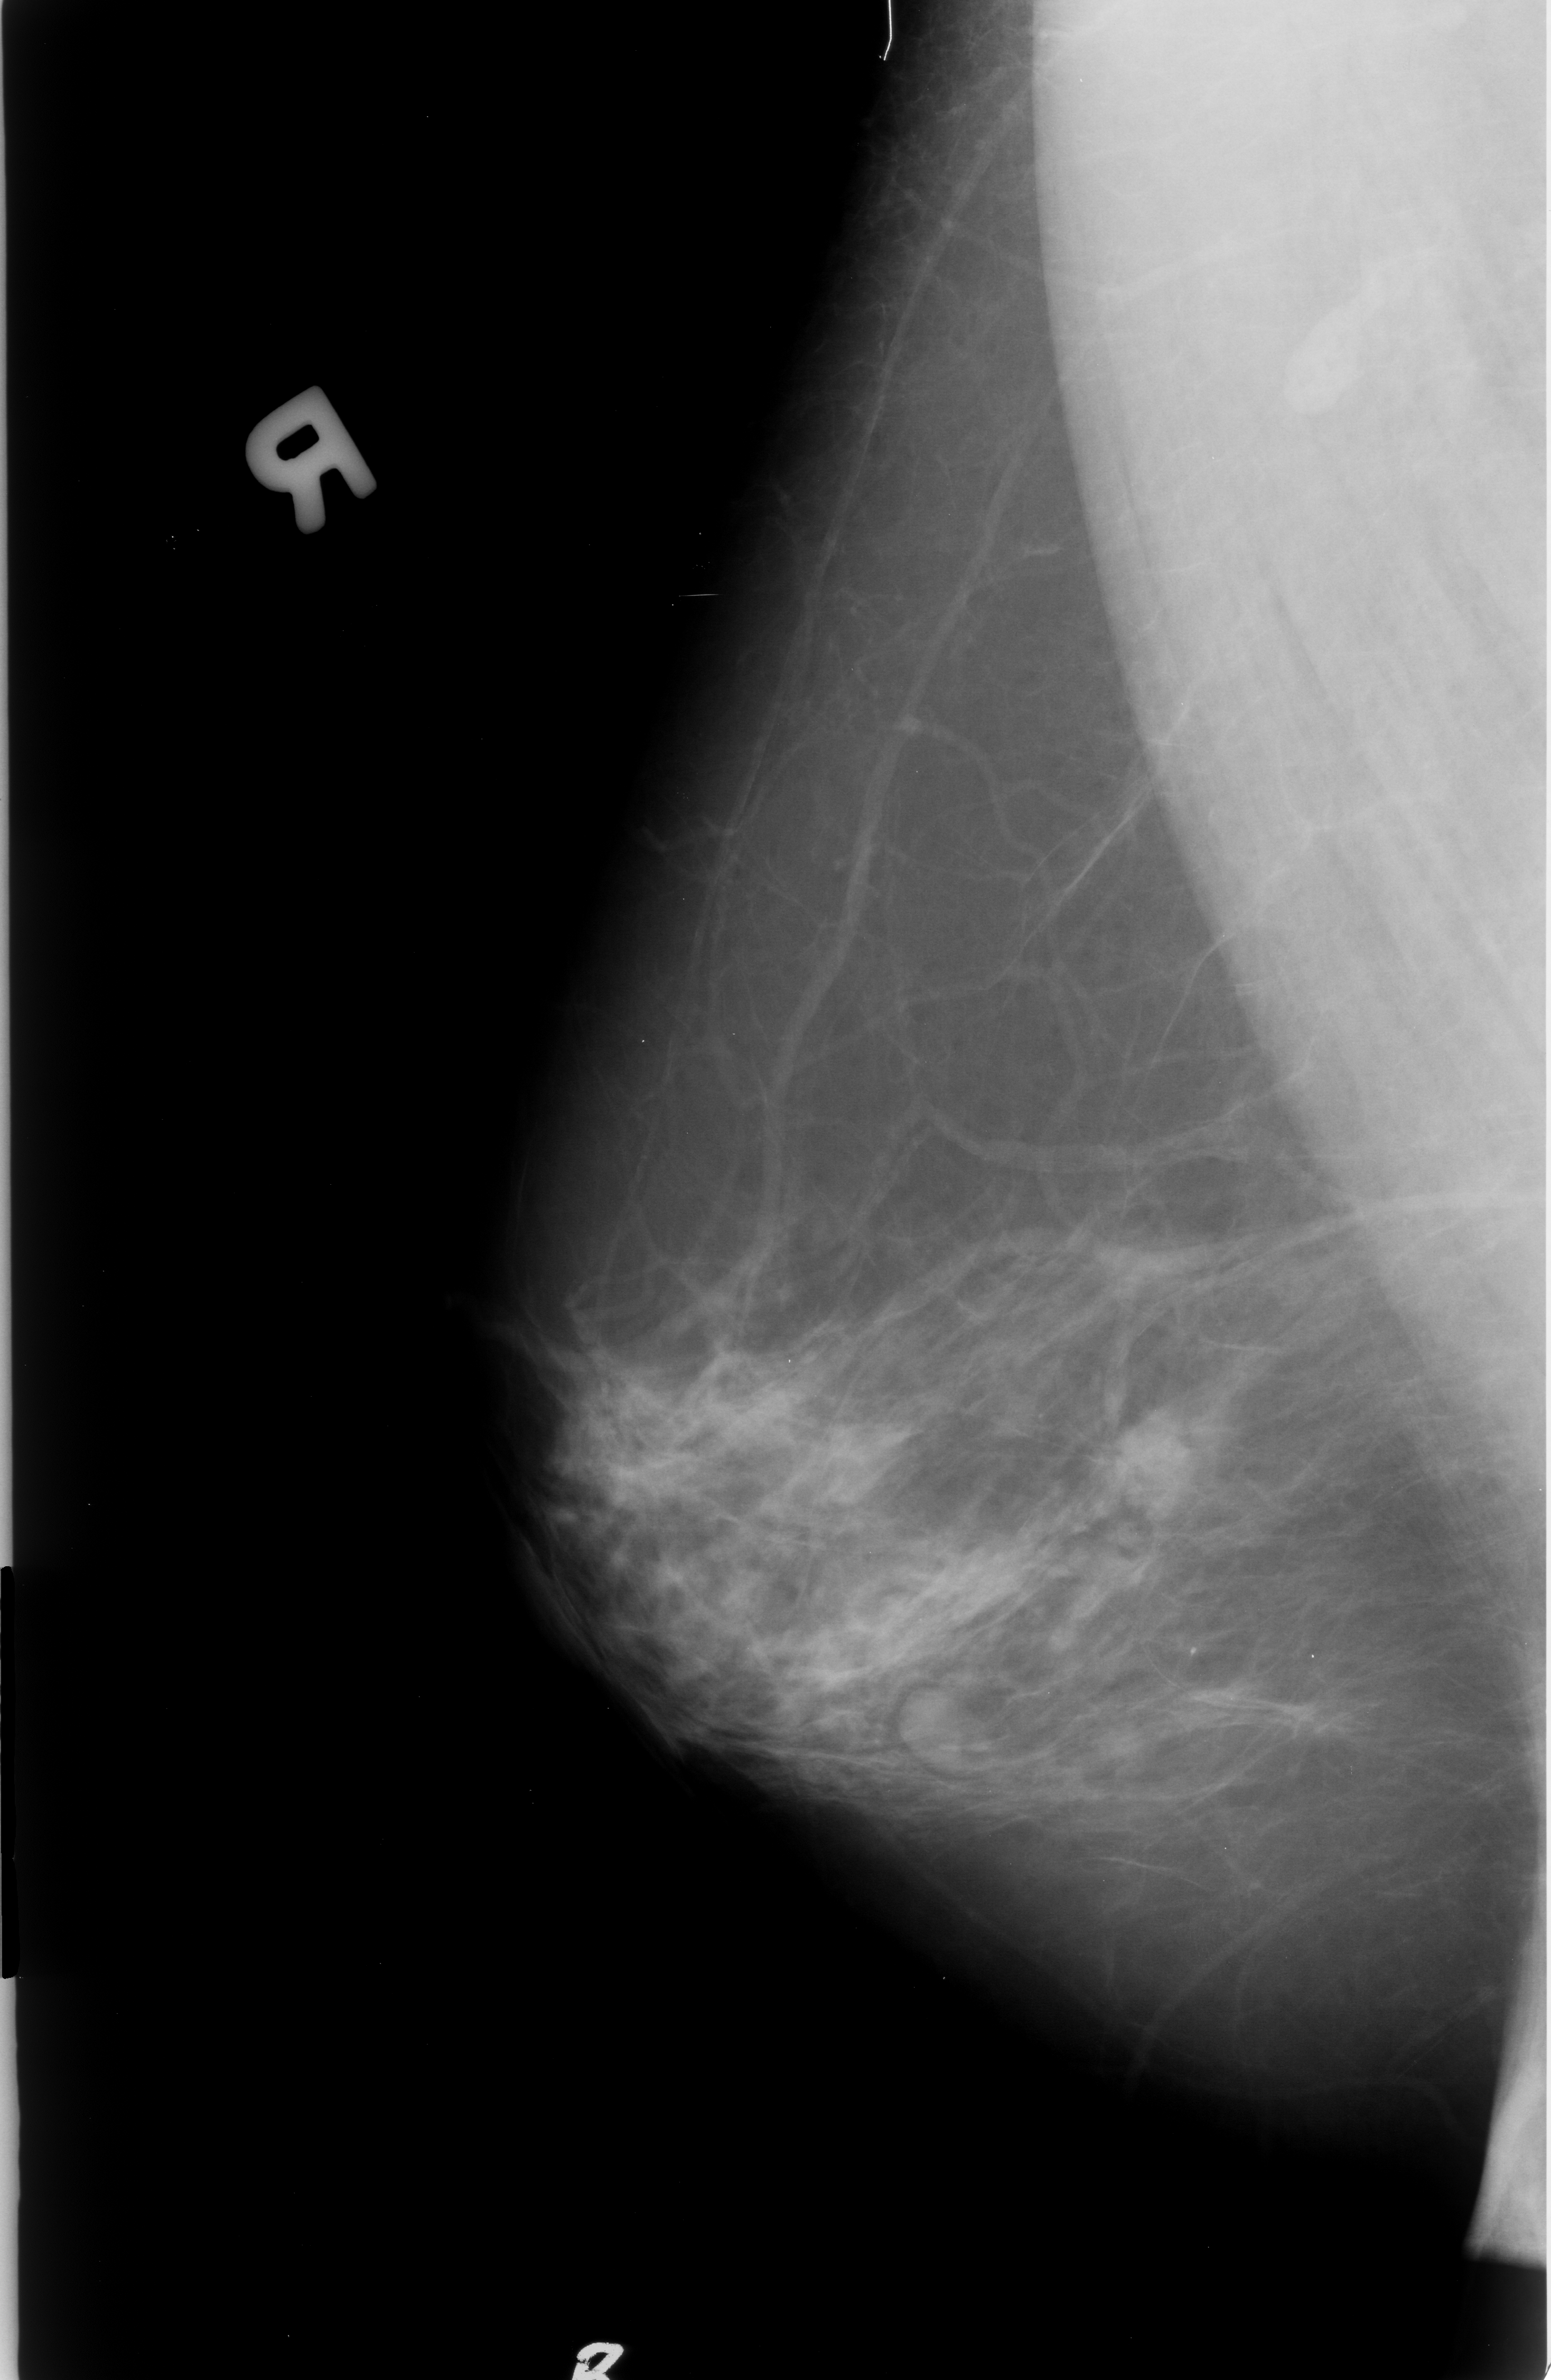
Scanned film-screen mammogram; right breast; MLO view; breast composition: scattered fibroglandular densities (BI-RADS density category 2 of 4); 1551 × 2380 image matrix.
Expert-marked regions of interest on this image (one box per marked abnormality):
- mass, shape irregular / architectural distortion, margins microlobulated / ill defined / spiculated; BI-RADS assessment category 4; subtlety rating 4 on a 1 (subtle) to 5 (obvious) scale; pathology result (as recorded, not read from the image): malignant: bounding box (x1, y1, x2, y2) in pixels: (1083, 1398, 1198, 1514)